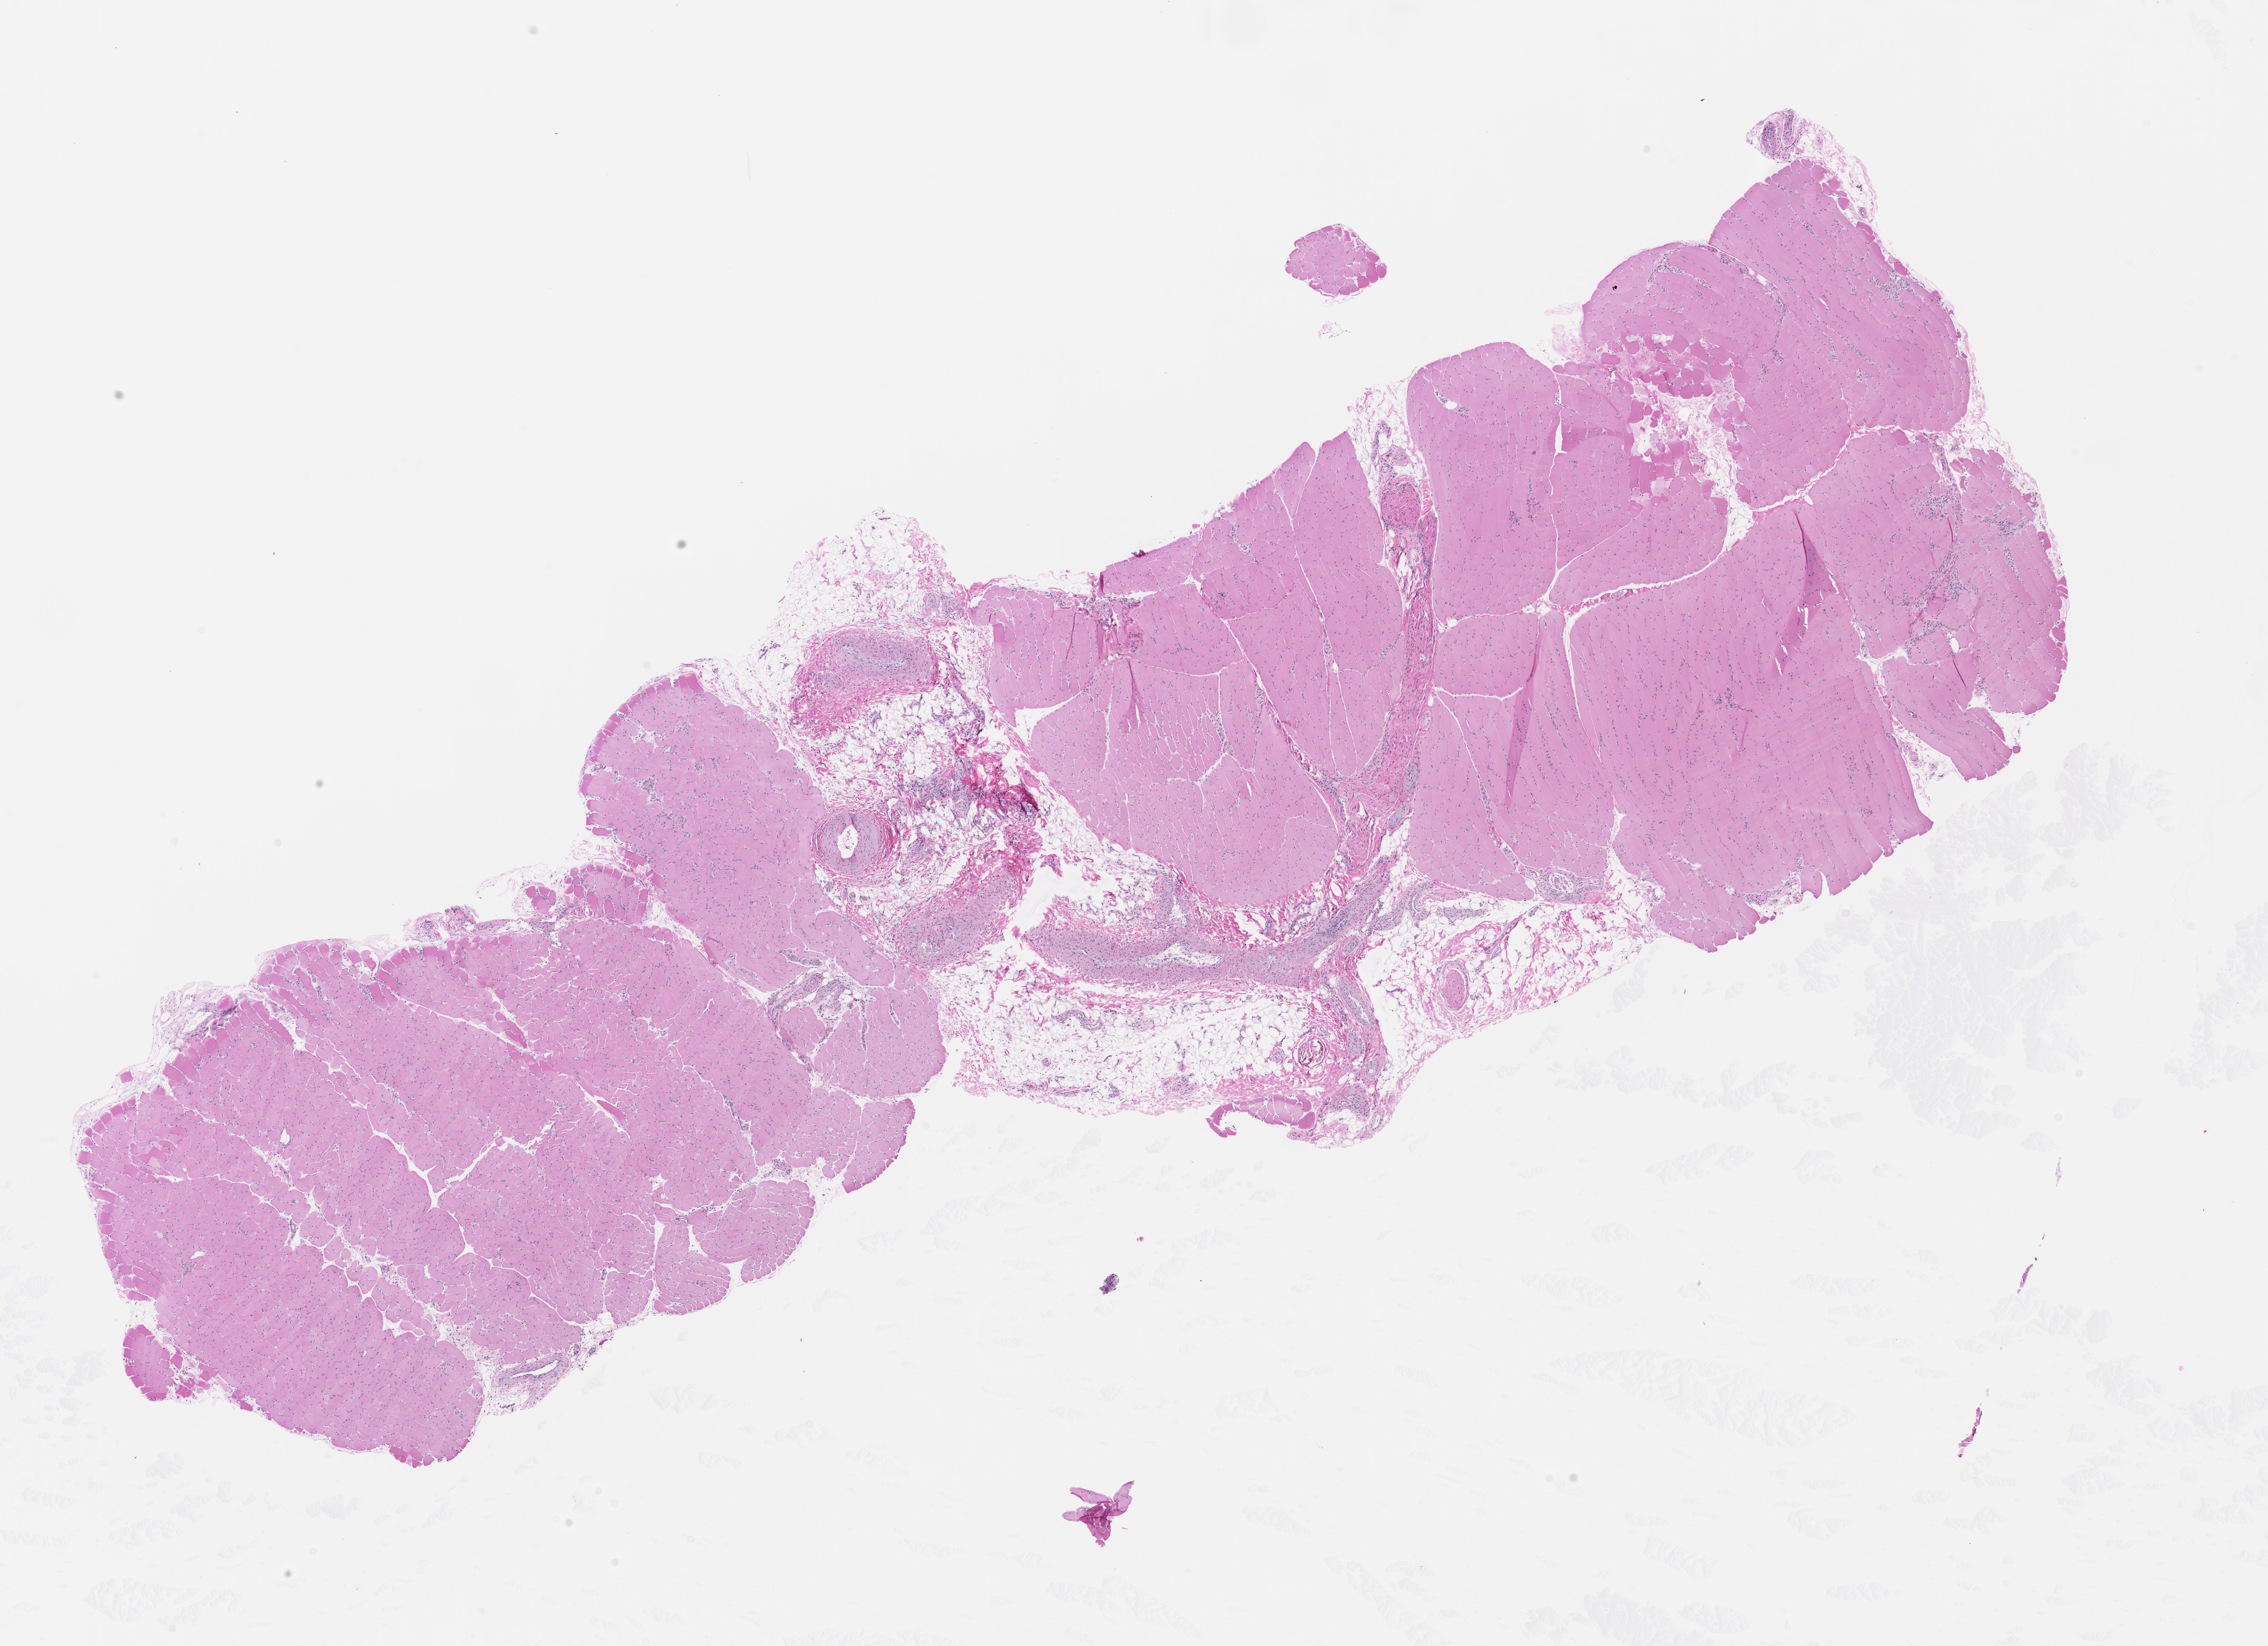
Whole-slide histology image, H&E-stained — a low-resolution overview of the entire scanned area, about 15.0 x 10.9 mm (from a 20x scan).
Patient diagnosis (cohort enrolment): sarcoma (site not recorded at cohort level).